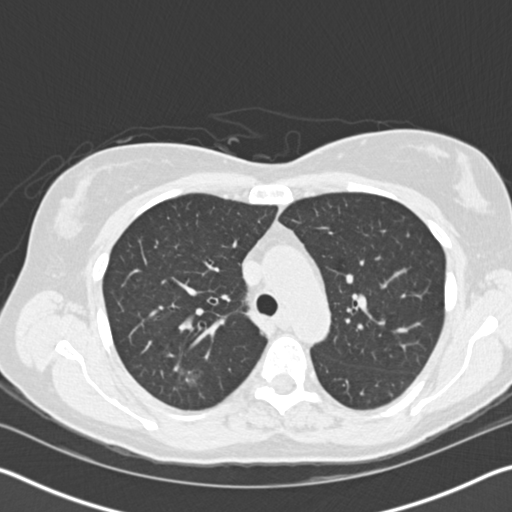
Axial slice from a low-dose chest CT screening exam, baseline annual screen, lung window (W 1500 / L -600 HU), standard (soft-tissue) reconstruction kernel (B30f), 120 kVp, 512 × 512 image matrix. Female, age 58 years at enrolment. Current smoker at enrolment.
- Expert-annotated lung lesion, bounding box (x1, y1, x2, y2) in pixels: (161, 349, 219, 405).
- The screening reader recorded 3 non-calcified nodules or masses ≥4 mm on this exam; which of them this box marks is not recorded.